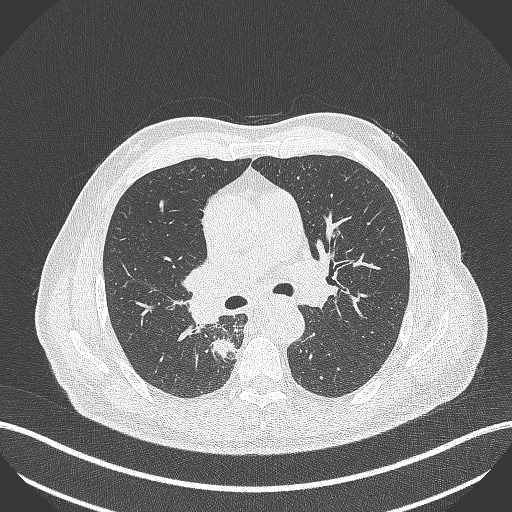
Chest CT, one axial slice. Slice 281 of 451 in the series (ordered by position). Lung window (W 1500 / L -600 HU). 1 mm slice thickness. 512 × 512 image matrix, field of view 400 × 400 mm. Patient: male, 61 years. From the clinical record (not read from this slice): clinical TNM (as recorded): T1 N0 M0; histopathological grade: G3.
Outlined on this slice (rectangle marked by the reading radiologist):
- lung tumour (recorded histology: small cell carcinoma): bounding box [x1, y1, x2, y2] px = [207, 335, 238, 360]